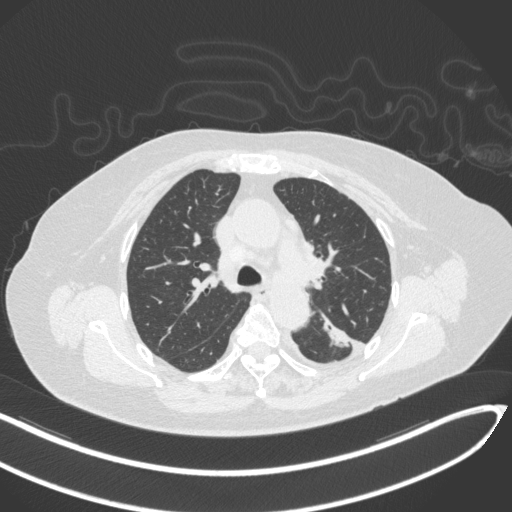
Chest CT, one axial slice; position 215 of 270 along the scan axis; reconstruction kernel B31f; lung window (W 1500 / L -600 HU); 512 × 512 image matrix, field of view 400 × 400 mm. Female patient, age 76 years. Case-level facts recorded for this patient, not image findings: clinical TNM (as recorded): T1c N0 M0.
Annotated regions visible in this slice (bounding box drawn by a radiologist):
- lung tumour (recorded histology: adenocarcinoma): box from (x=323, y=312) to (x=349, y=352) px